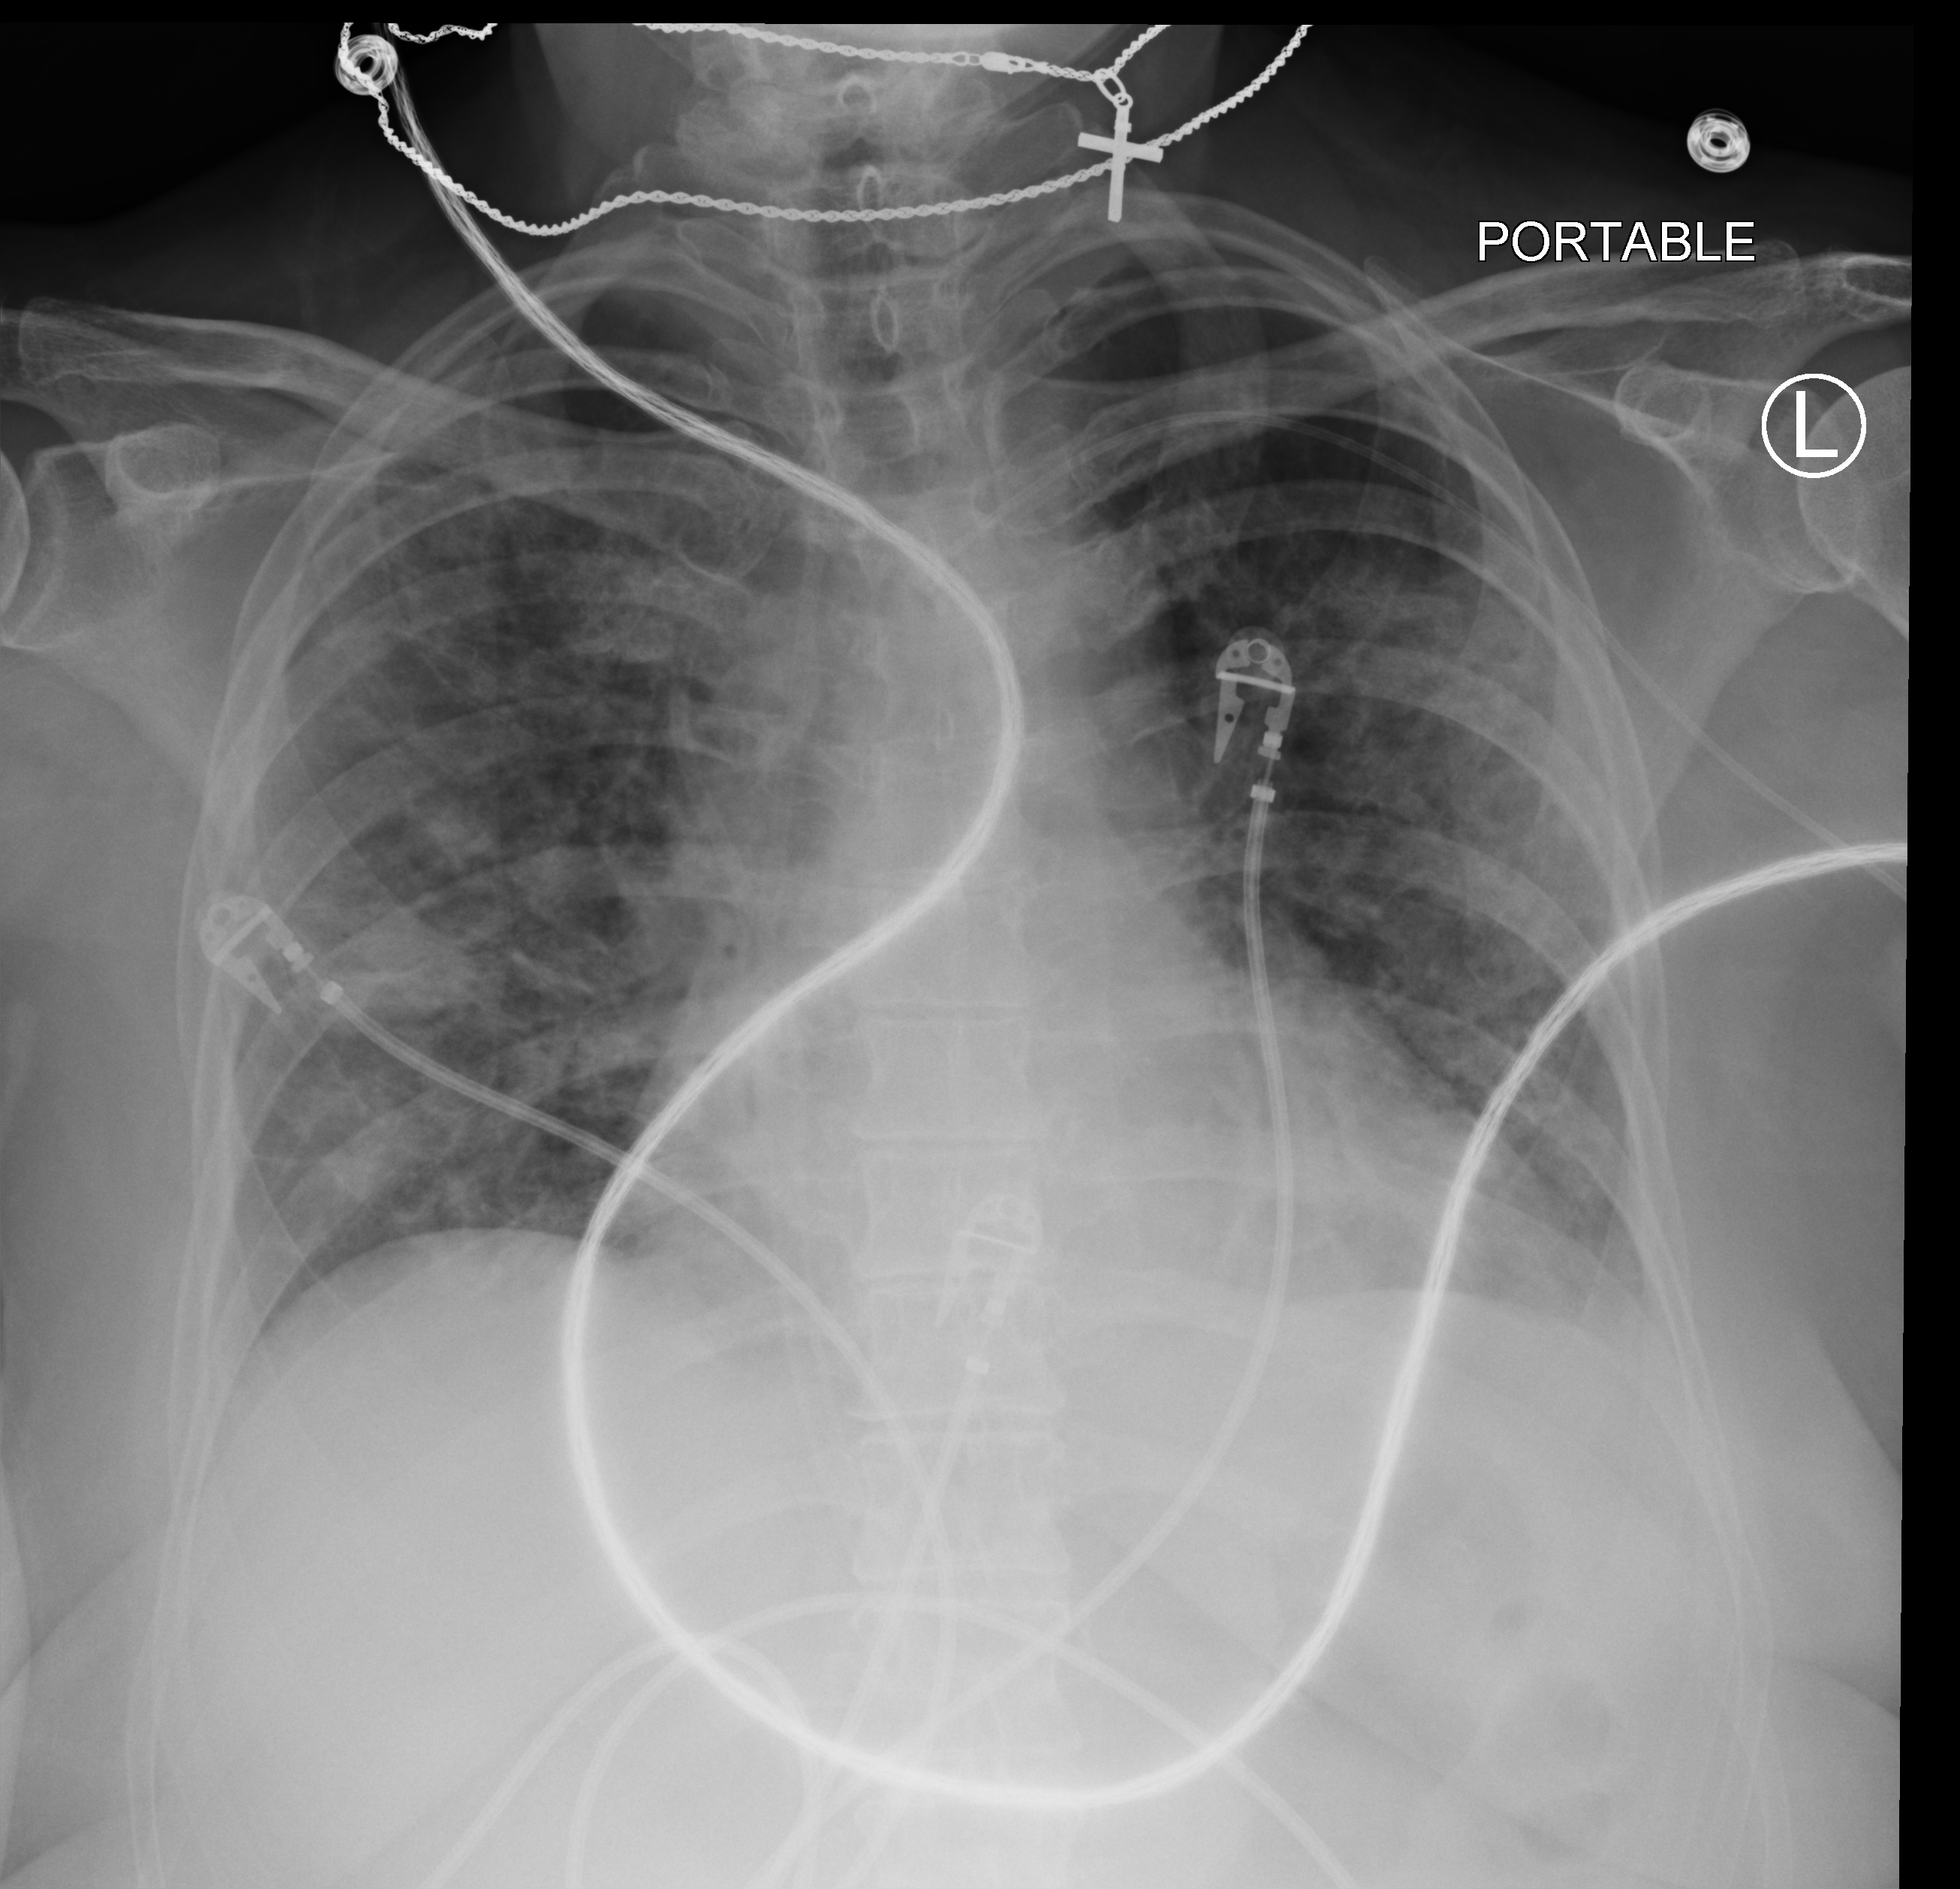
Bedside chest radiograph (computed radiography); anteroposterior (AP) projection. Female patient hospitalised with COVID-19, age 18–59 years.
Admission-level facts for this patient (not findings on this image; timing relative to this image not recorded): admitted to intensive care during this hospital stay: yes; chronic kidney disease (admission record): no; length of hospital stay: 20 days.